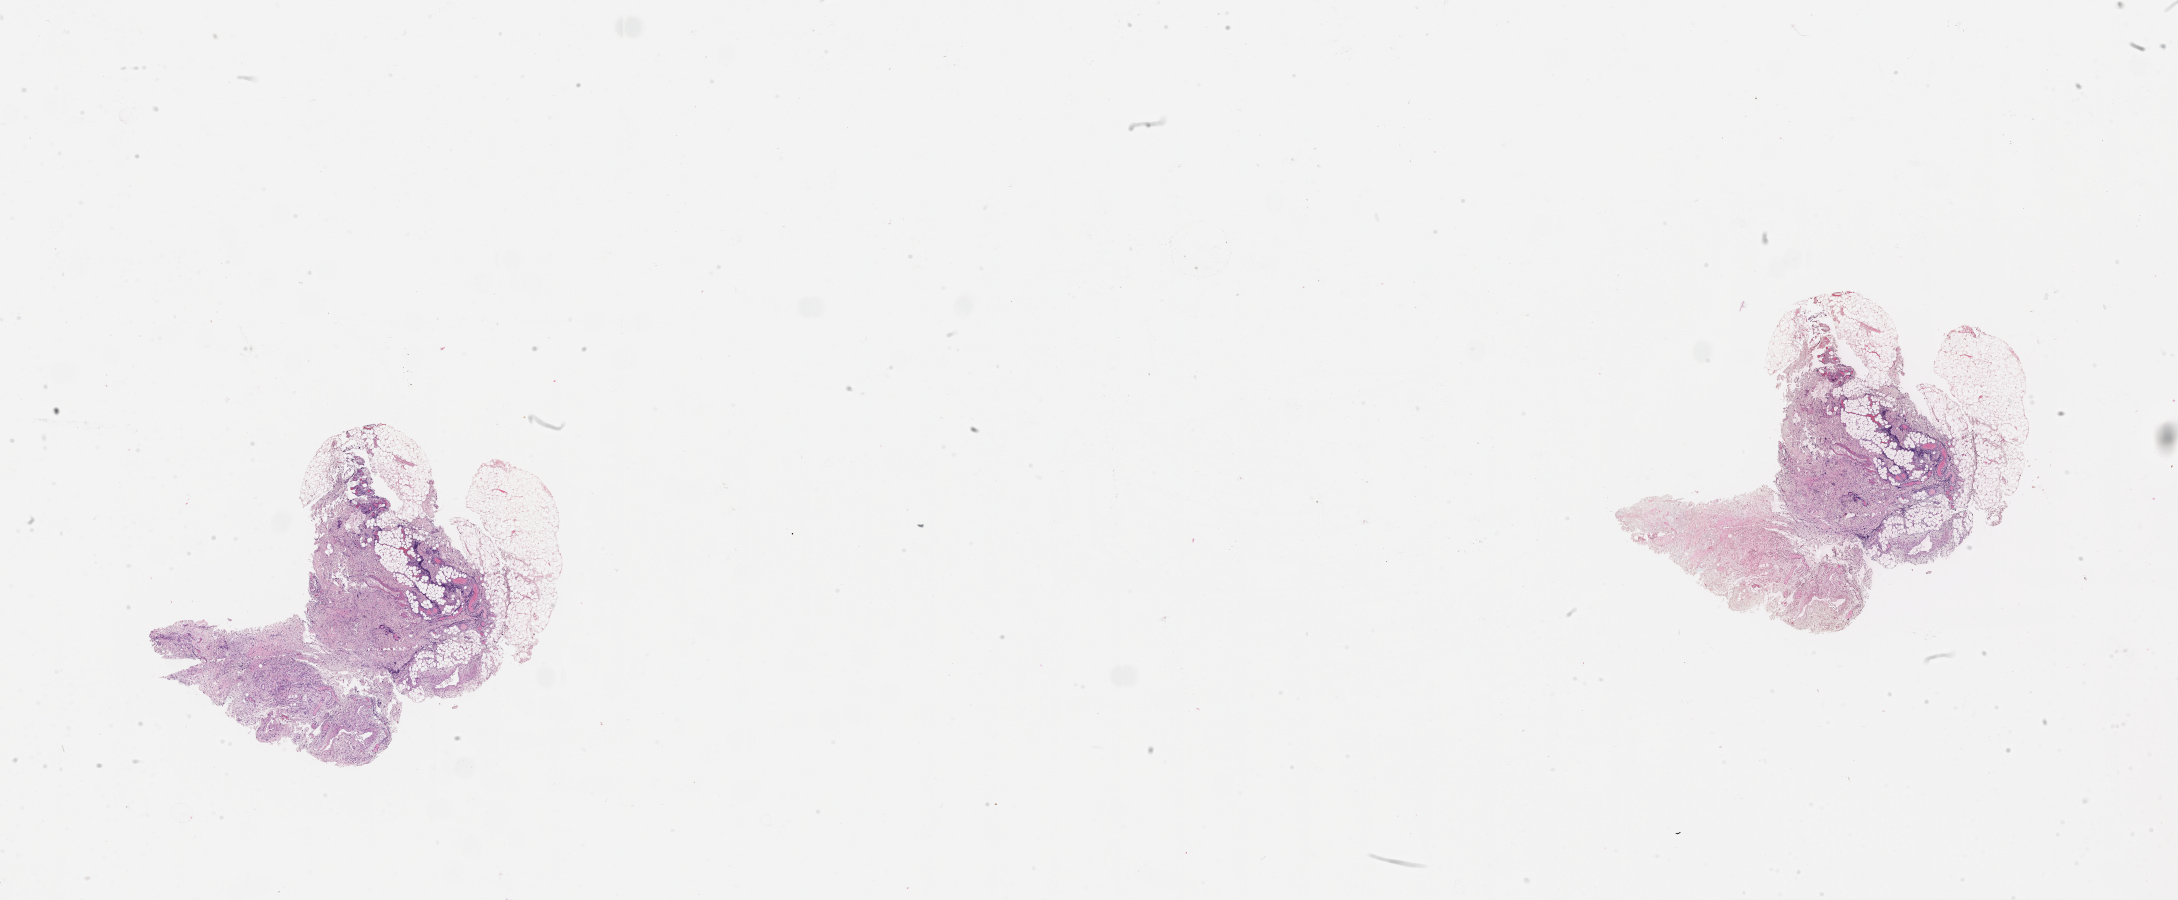
Digitized Hematoxylin and eosin (H&E) stained tissue section (whole slide), whole scanned area (about 35.1 x 14.5 mm, slide scanned at 20x) shown as a low-resolution overview. Pancreas, tumour tissue. 69-year-old male patient. Histologic grade: G2 (moderately differentiated).
* AJCC pathologic stage: IA
* histologic diagnosis: Infiltrating duct carcinoma, NOS
* primary tumour site (as recorded): head